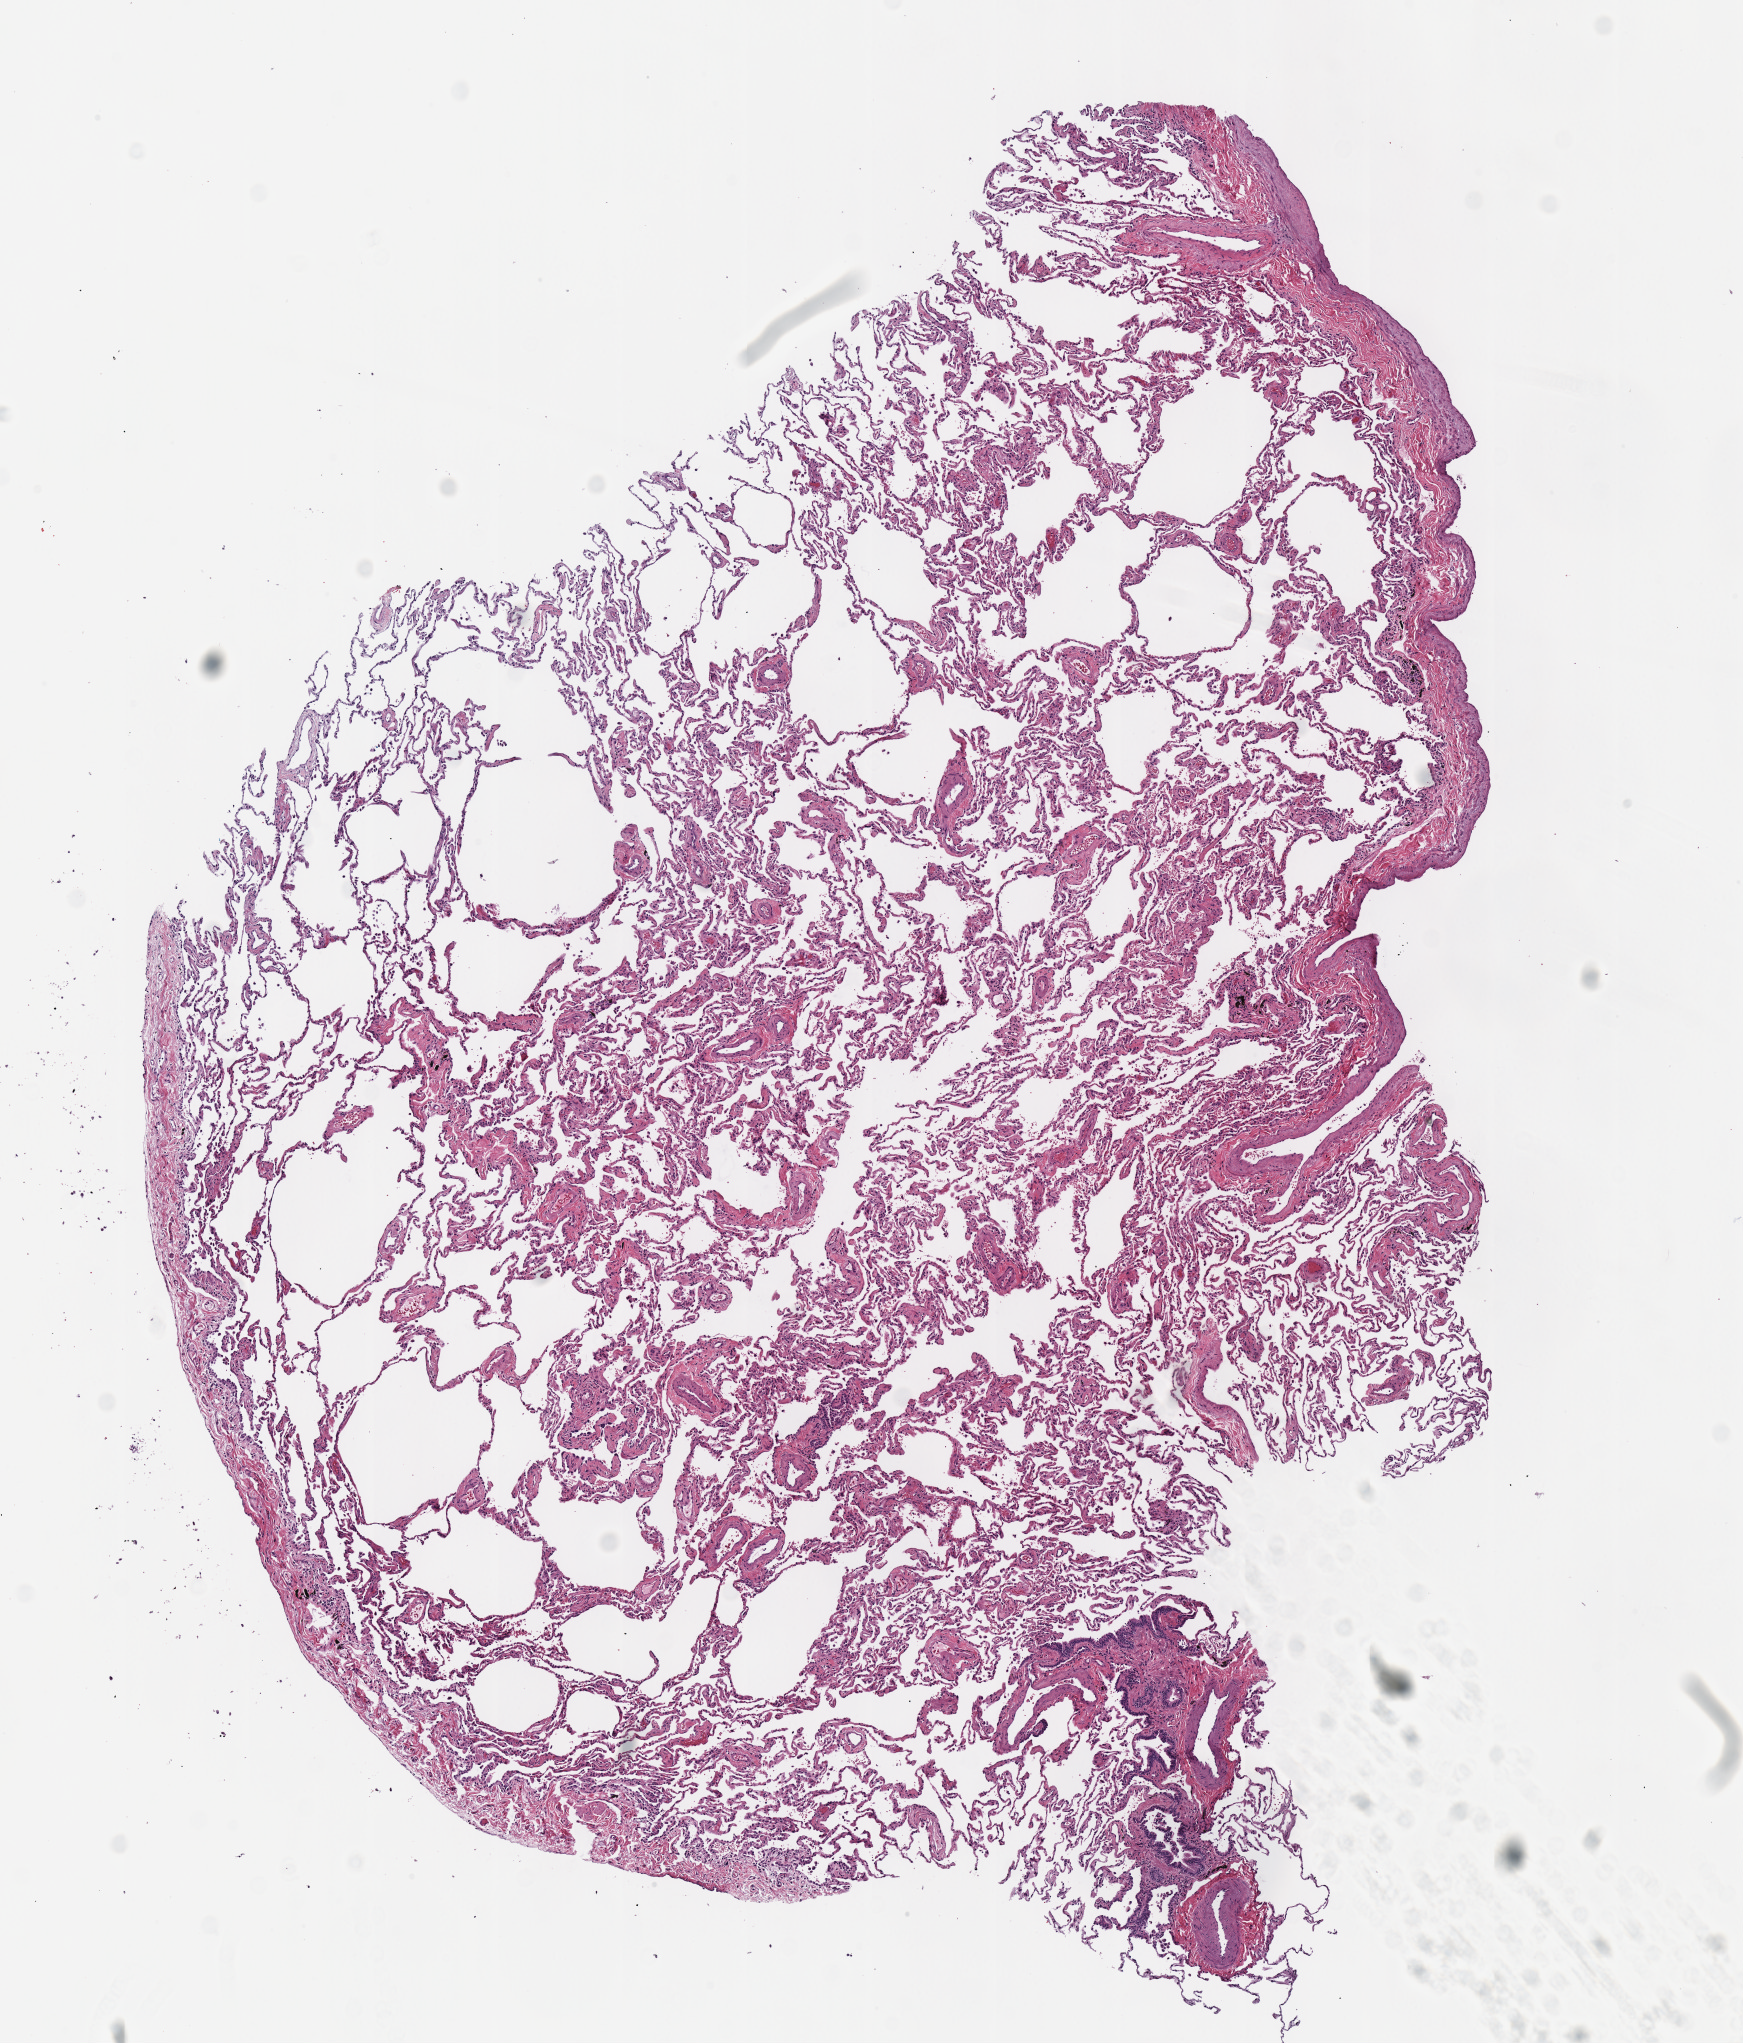
Digitized Hematoxylin and eosin (H&E) stained tissue section (whole slide), low-resolution overview of the scanned area, about 6.9 x 8.0 mm; frozen section from the top of the tissue portion; lung, solid tissue normal (non-tumour tissue) sample. Patient: male, age at initial diagnosis 64 years.
This section: solid tissue normal (non-tumour) sample from the same patient. Patient diagnosis: Adenocarcinoma with mixed subtypes (middle lobe, lung).